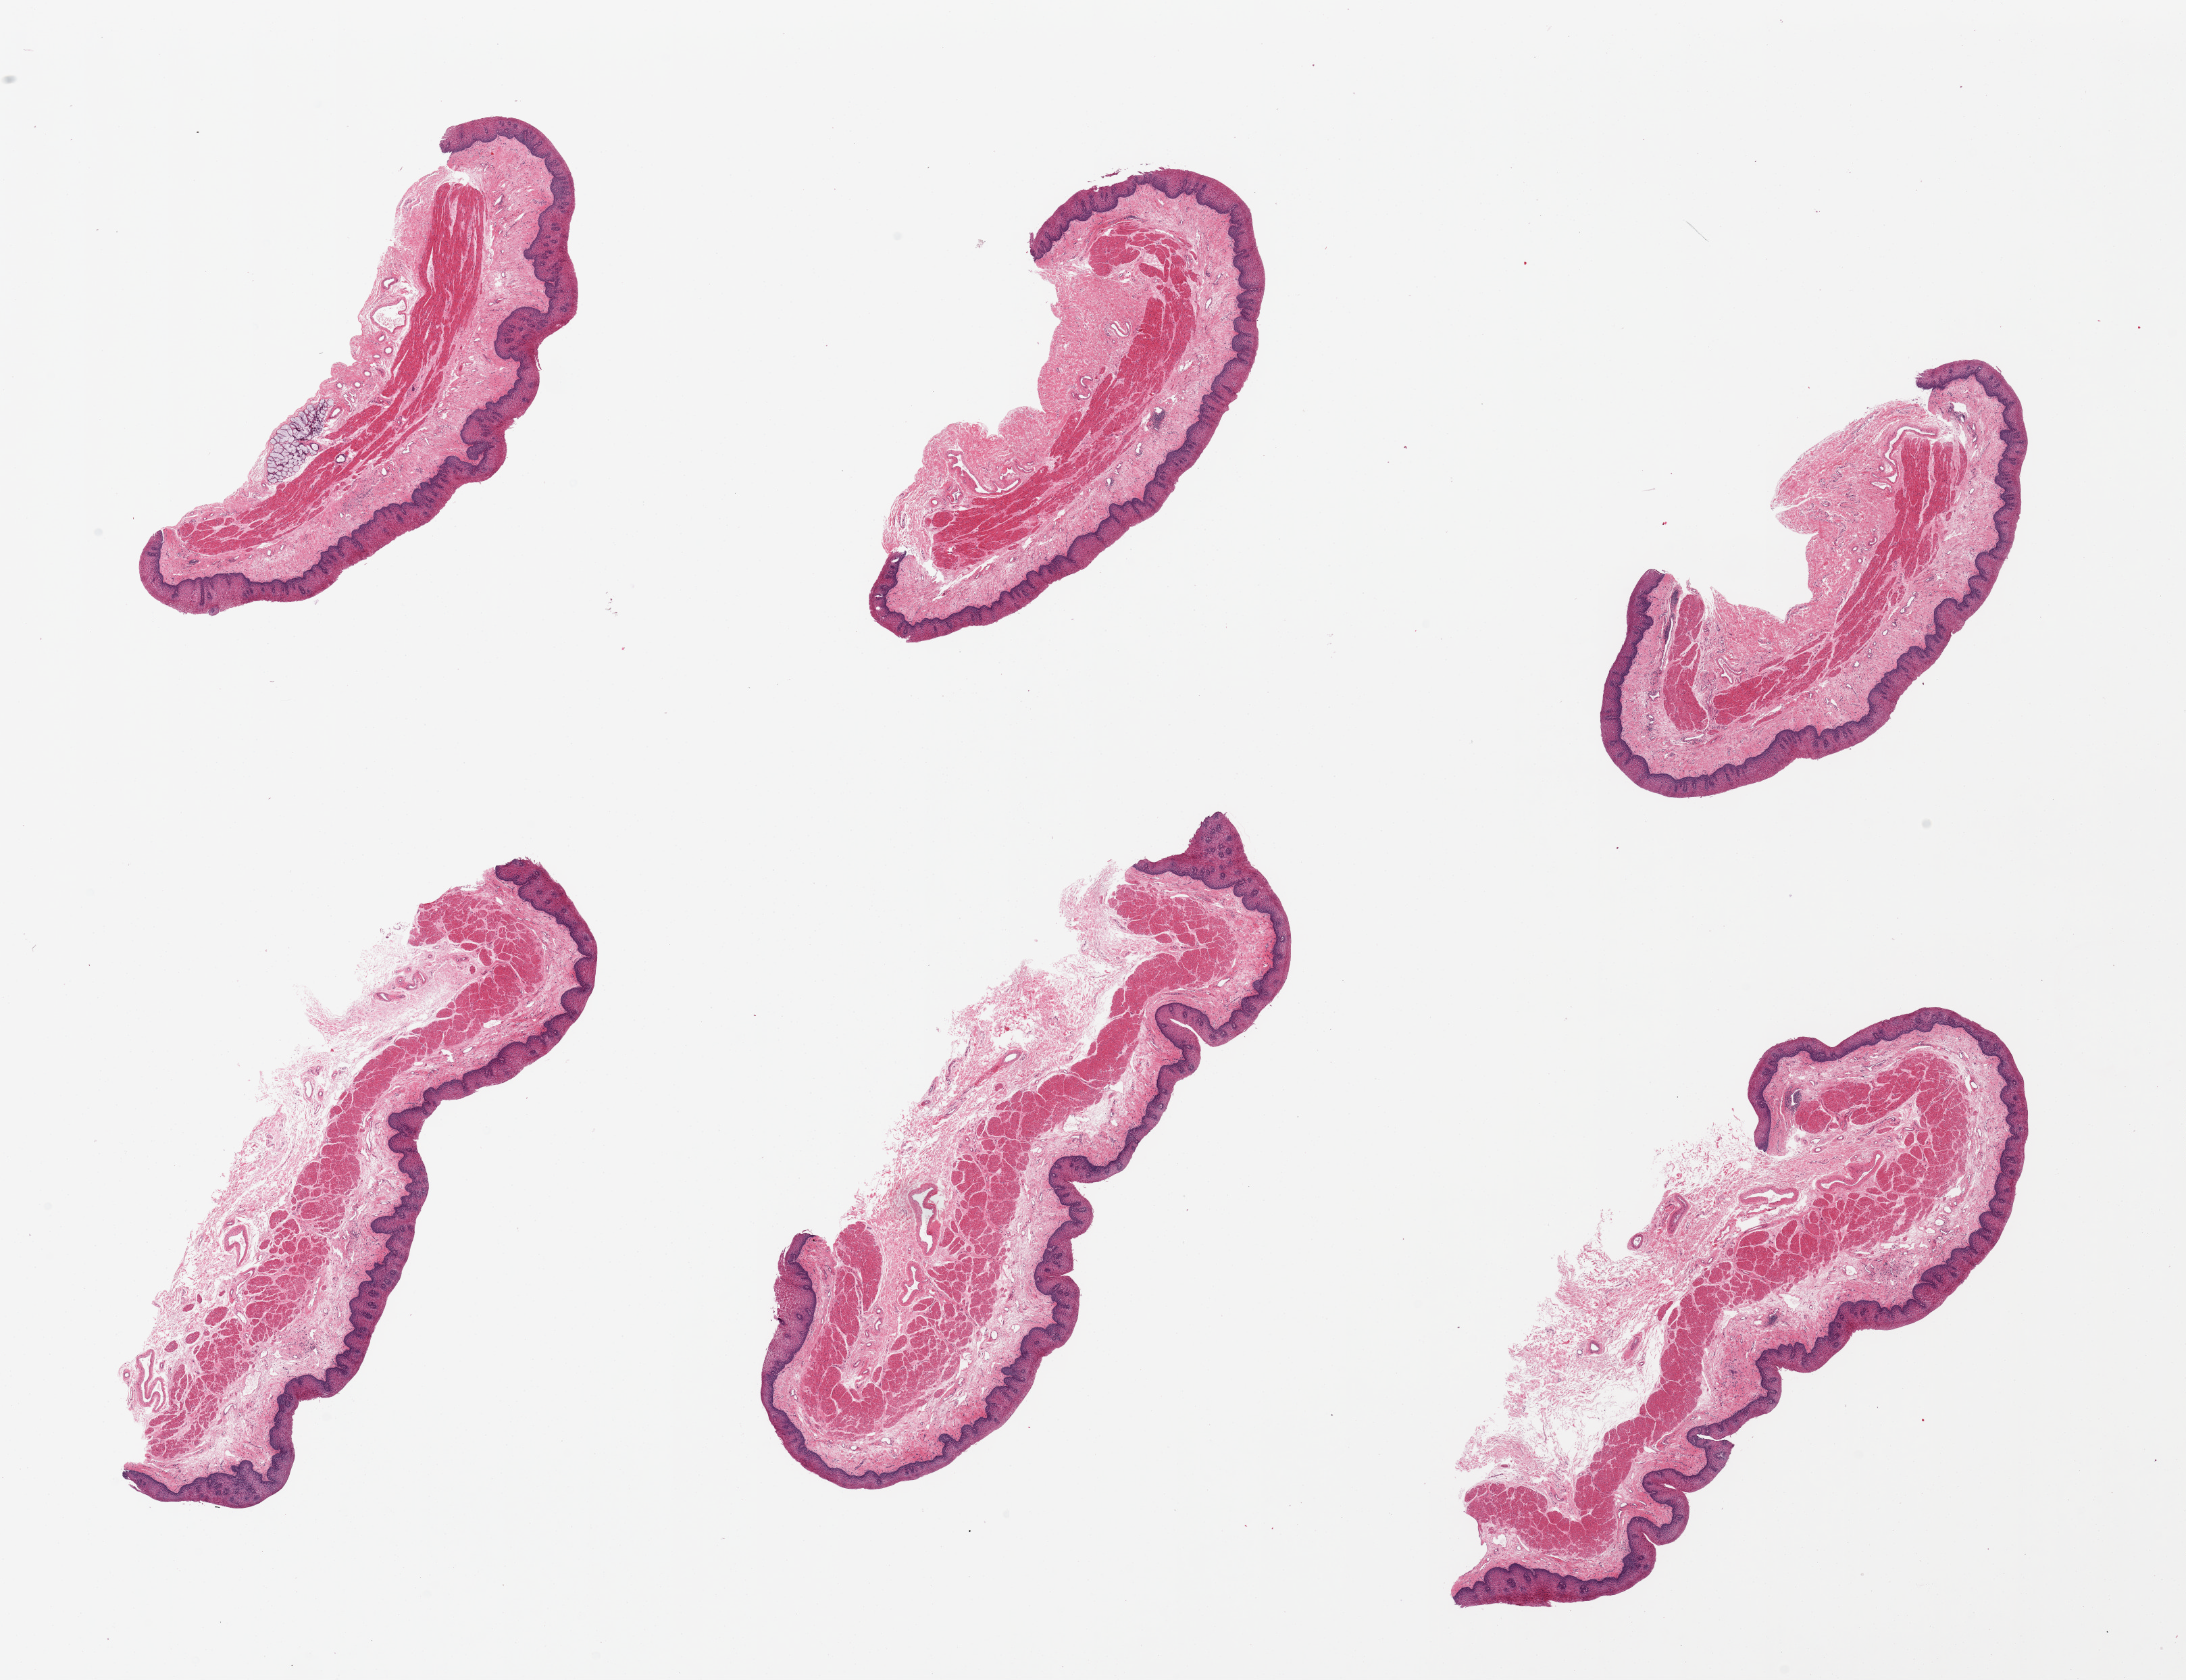
Whole-slide image, hematoxylin and eosin (H&E) stain — a low-resolution overview of the entire scanned area, about 25.6 x 19.7 mm, PAXgene-fixed paraffin-embedded (PFPE) section, target tissue: esophageal mucous membrane, donor tissue sample.
Reviewer comment on this tissue sample: 6 pieces. Well dissected.